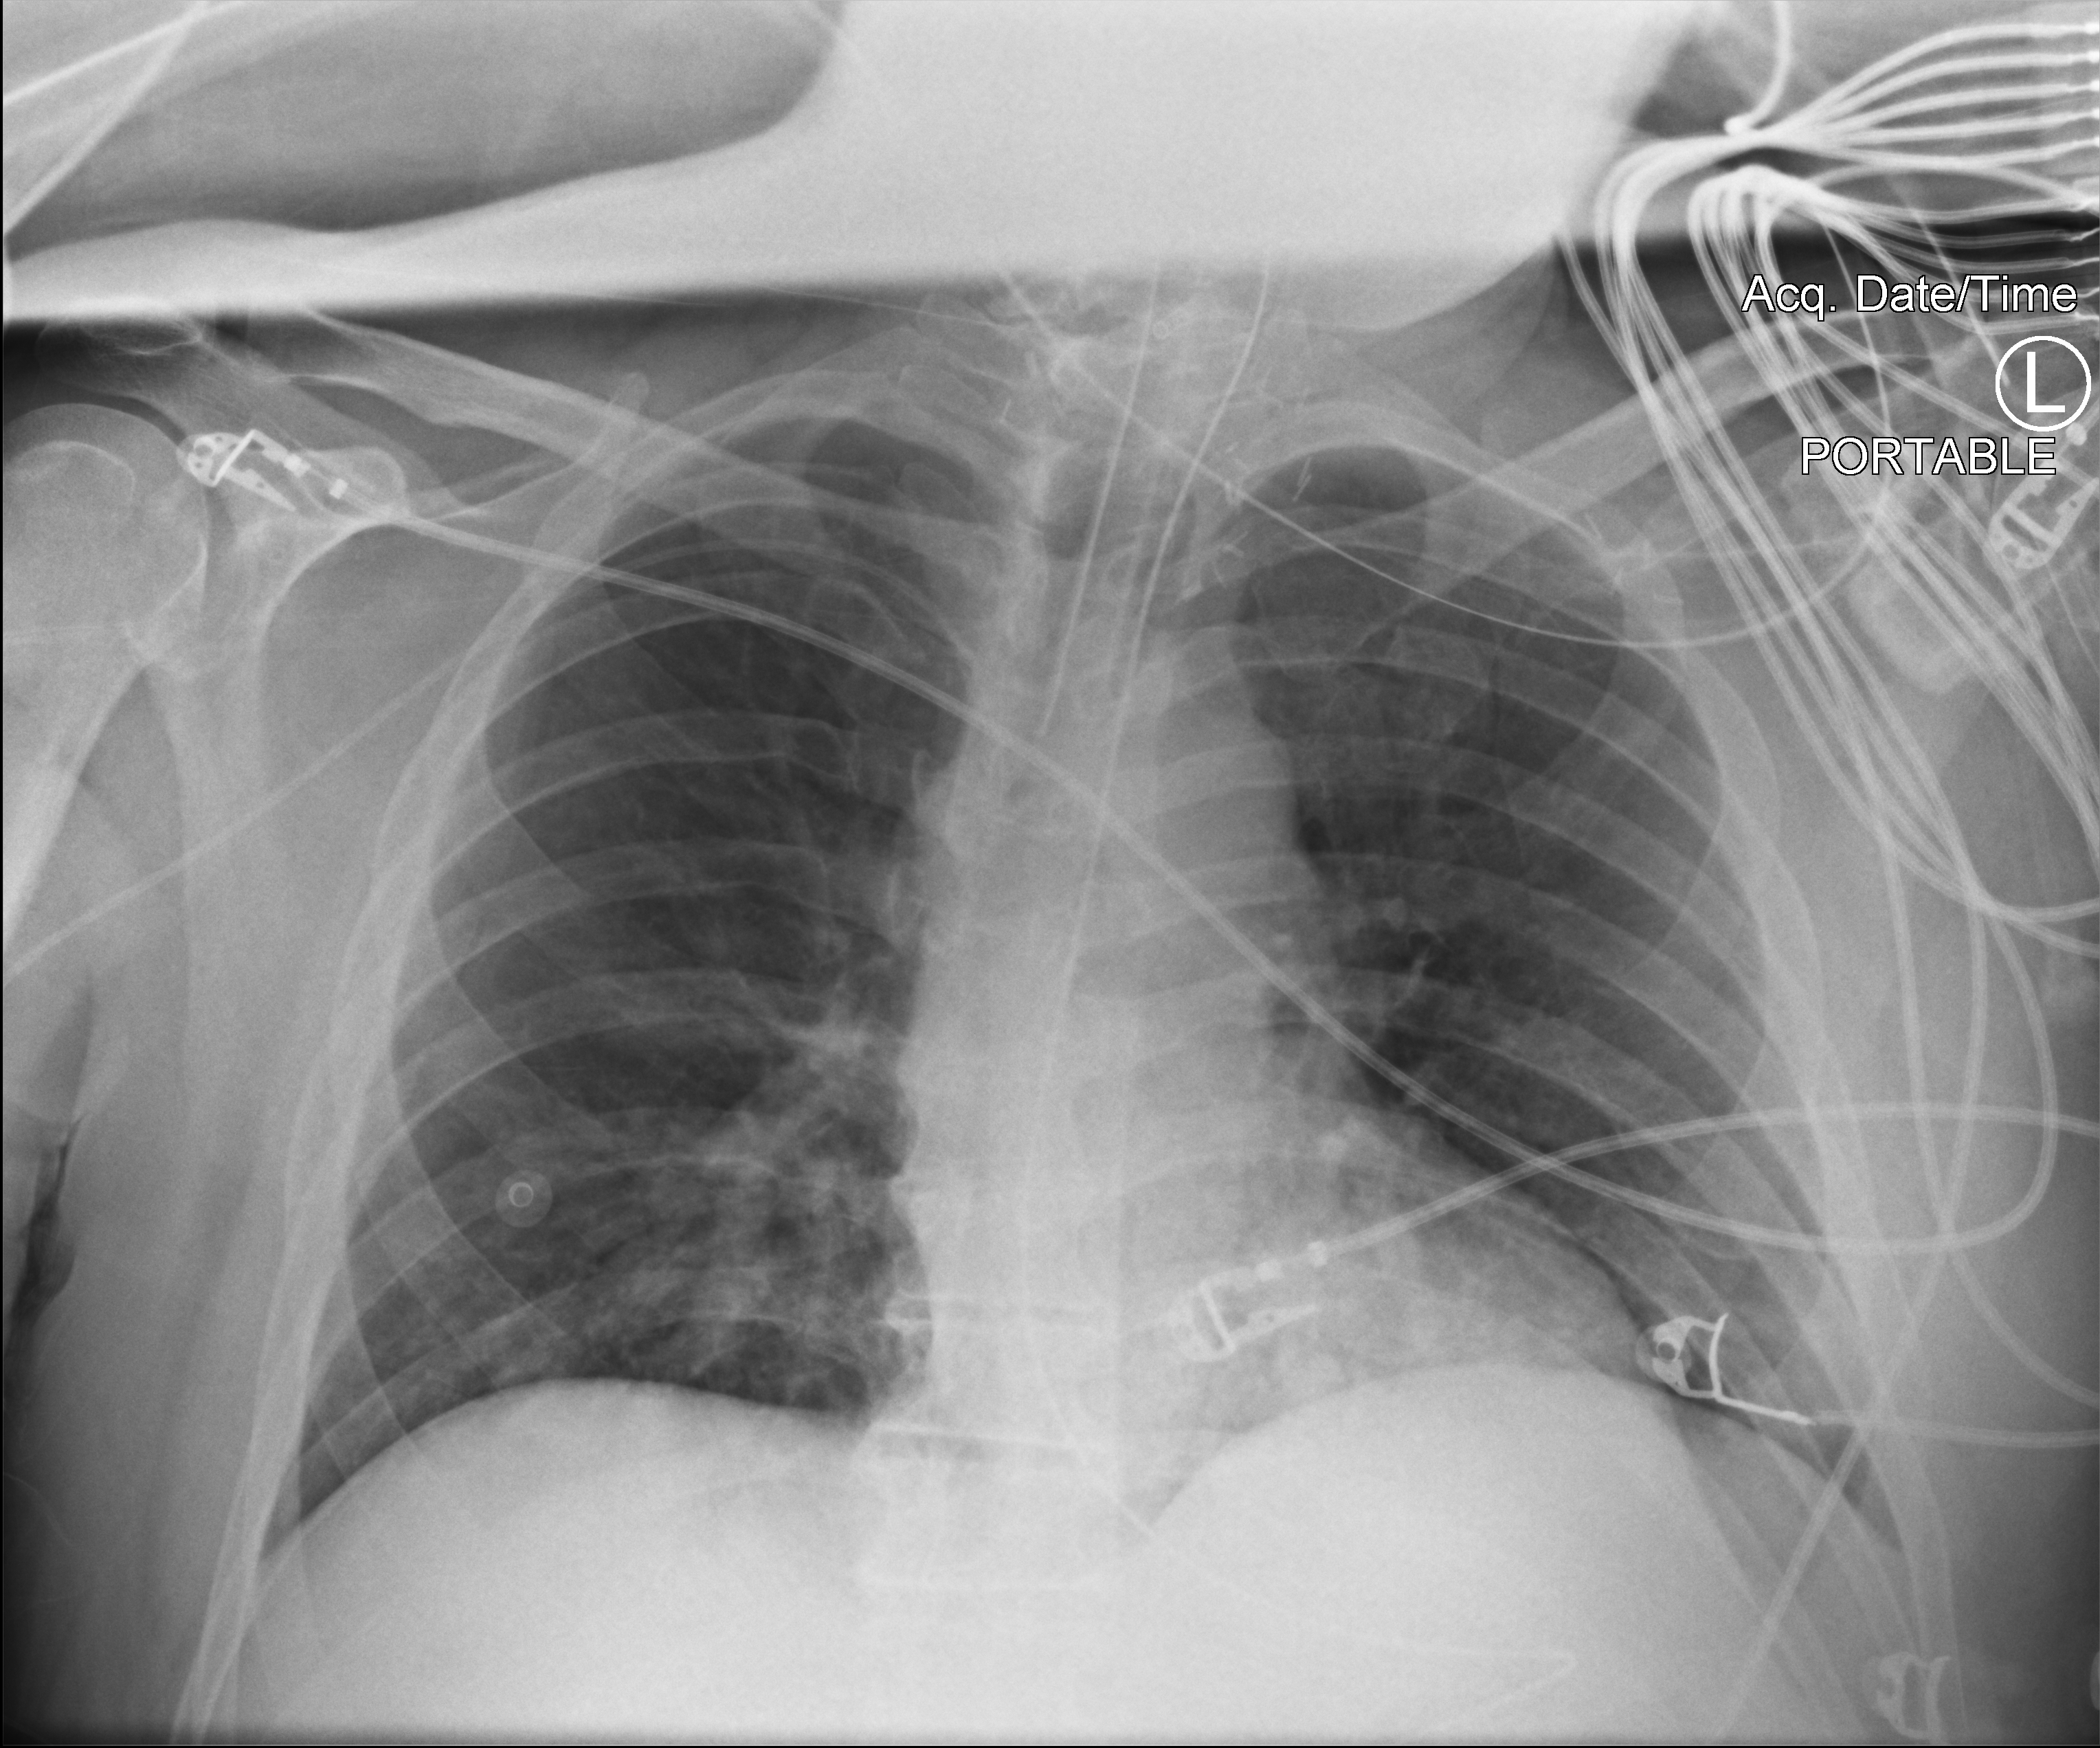
Bedside chest radiograph (computed radiography), anteroposterior (AP) projection. Adult patient hospitalised with COVID-19, age 18–59 years.
Hospital-stay facts (about this admission, not read from this image; timing relative to this image not recorded): admitted to intensive care during this hospital stay: yes.